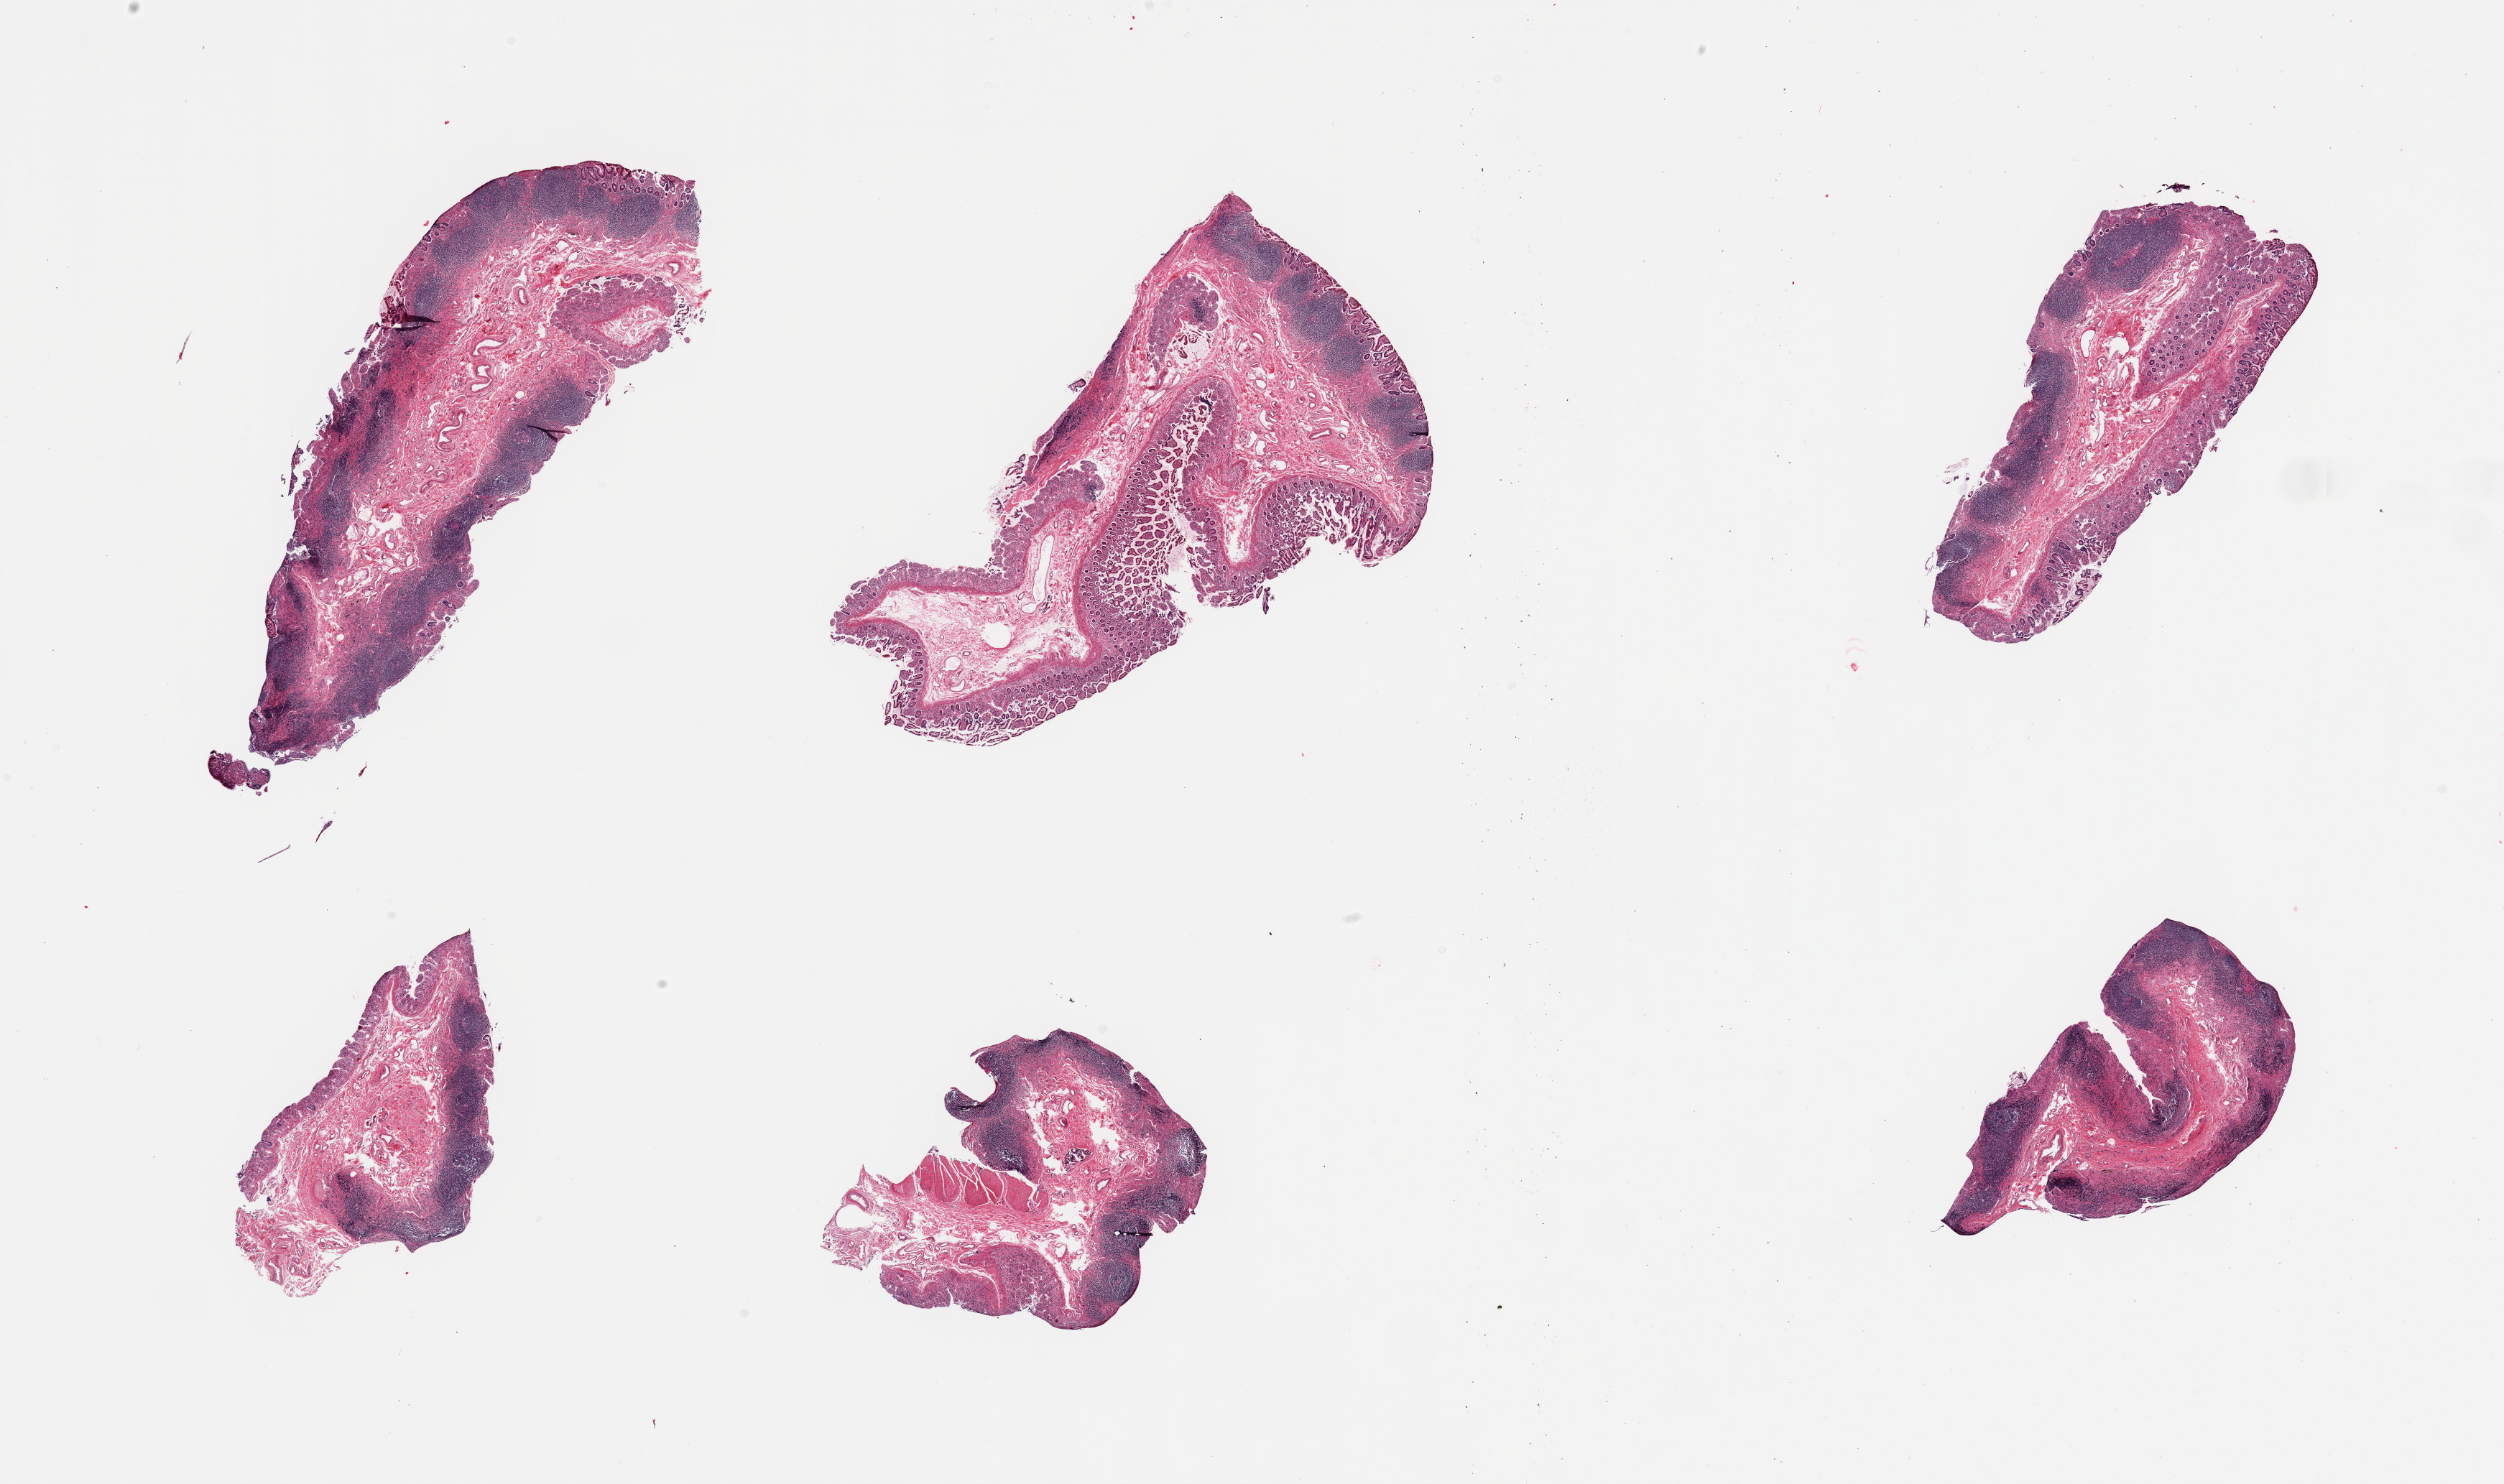
Hematoxylin and eosin (H&E) whole-slide image, brightfield — shown as a low-resolution overview of the whole scanned area (about 27.6 x 16.3 mm, acquisition: 20x scan); PAXgene-fixed paraffin-embedded (PFPE) section; section of ileum (target tissue); donor tissue sample. Female donor.
Reviewer comment on this tissue sample: 6 pieces; predominantly partially autolyzed mucosa and submucosa with good (but variable) lymphoid component, small portion of muscularis in 1 piece.